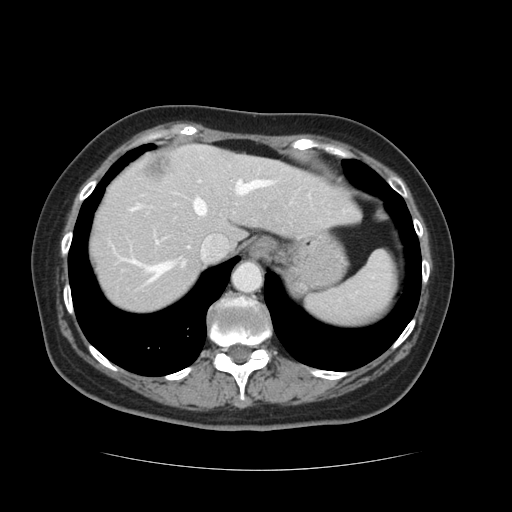
Contrast-enhanced abdominal CT, one axial slice. Position 103 of 128 along the scan axis. 120 kVp. Intravenous contrast given. Soft-tissue window (W 400 / L 40 HU). 2.5 mm slice thickness. 512 × 512 image matrix, field of view 366 × 366 mm. Female patient, age 67 years. Case-level facts recorded for this patient, not image findings: diagnosis: colorectal cancer liver metastases, imaged before liver resection; multiple liver metastases: yes; largest metastasis: 3 cm.
Annotated regions visible in this slice (outlined manually by an expert reader):
- hepatic veins: bounding box (x1, y1, x2, y2) in pixels: (127, 180, 272, 285)
- liver: (88, 145, 356, 312)
- planned liver remnant (the part of the liver to remain after resection): (89, 157, 356, 312)
- portal vein (with intrahepatic branches): (198, 179, 202, 182)
- liver metastasis: (144, 158, 168, 181)